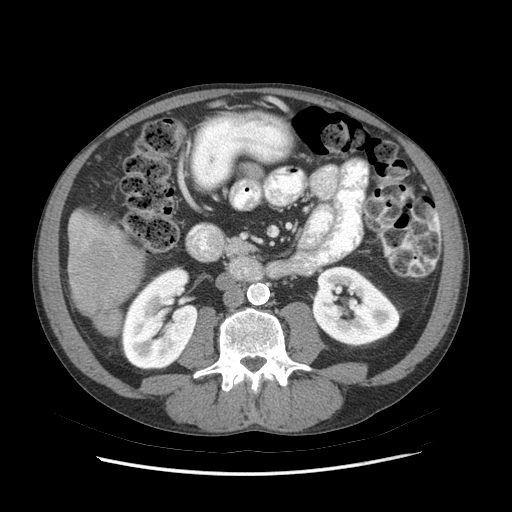
Contrast-enhanced abdominal CT (liver protocol), one axial slice; slice 17 of 89 in the series (ordered by position); soft-tissue window (W 400 / L 40 HU); 512 × 512 image matrix, field of view 380 × 380 mm. From the clinical record (not read from this slice): diagnosis: hepatocellular carcinoma (patient treated with transarterial chemoembolisation; whether this scan precedes or follows treatment is not stated here); TNM stage (as recorded): Stage-IIIB; Child-Pugh class: A; tumour nodularity: multinodular.
Annotated regions visible in this slice (semi-automatically segmented with operator editing):
- liver parenchyma outside the tumour (the mass and vessels are separate outlines, so this box may not span the whole liver): bounding box <68,210,144,334> (left, top, right, bottom; pixels)
- mass: <70,238,139,317>